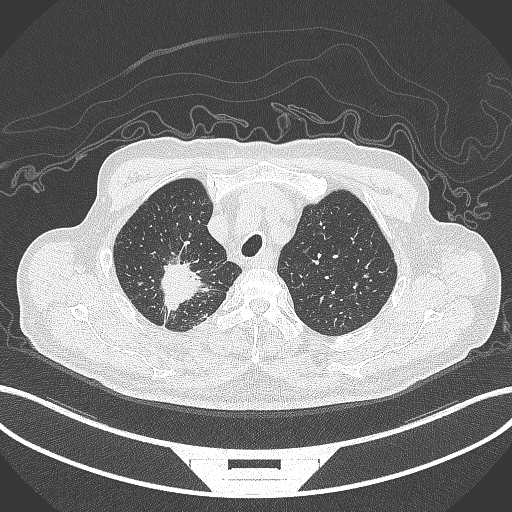
Chest CT, one axial slice. Reconstruction kernel B70f. Lung window (W 1500 / L -600 HU). 1 mm slice thickness. 512 × 512 image matrix. Male patient, age 69 years. Case-level facts recorded for this patient, not image findings: clinical TNM (as recorded): T1c N1 M1.
Annotated regions visible in this slice (bounding box drawn by a radiologist):
- lung tumour (recorded histology: adenocarcinoma): bounding box [x1, y1, x2, y2] px = [153, 253, 212, 311]